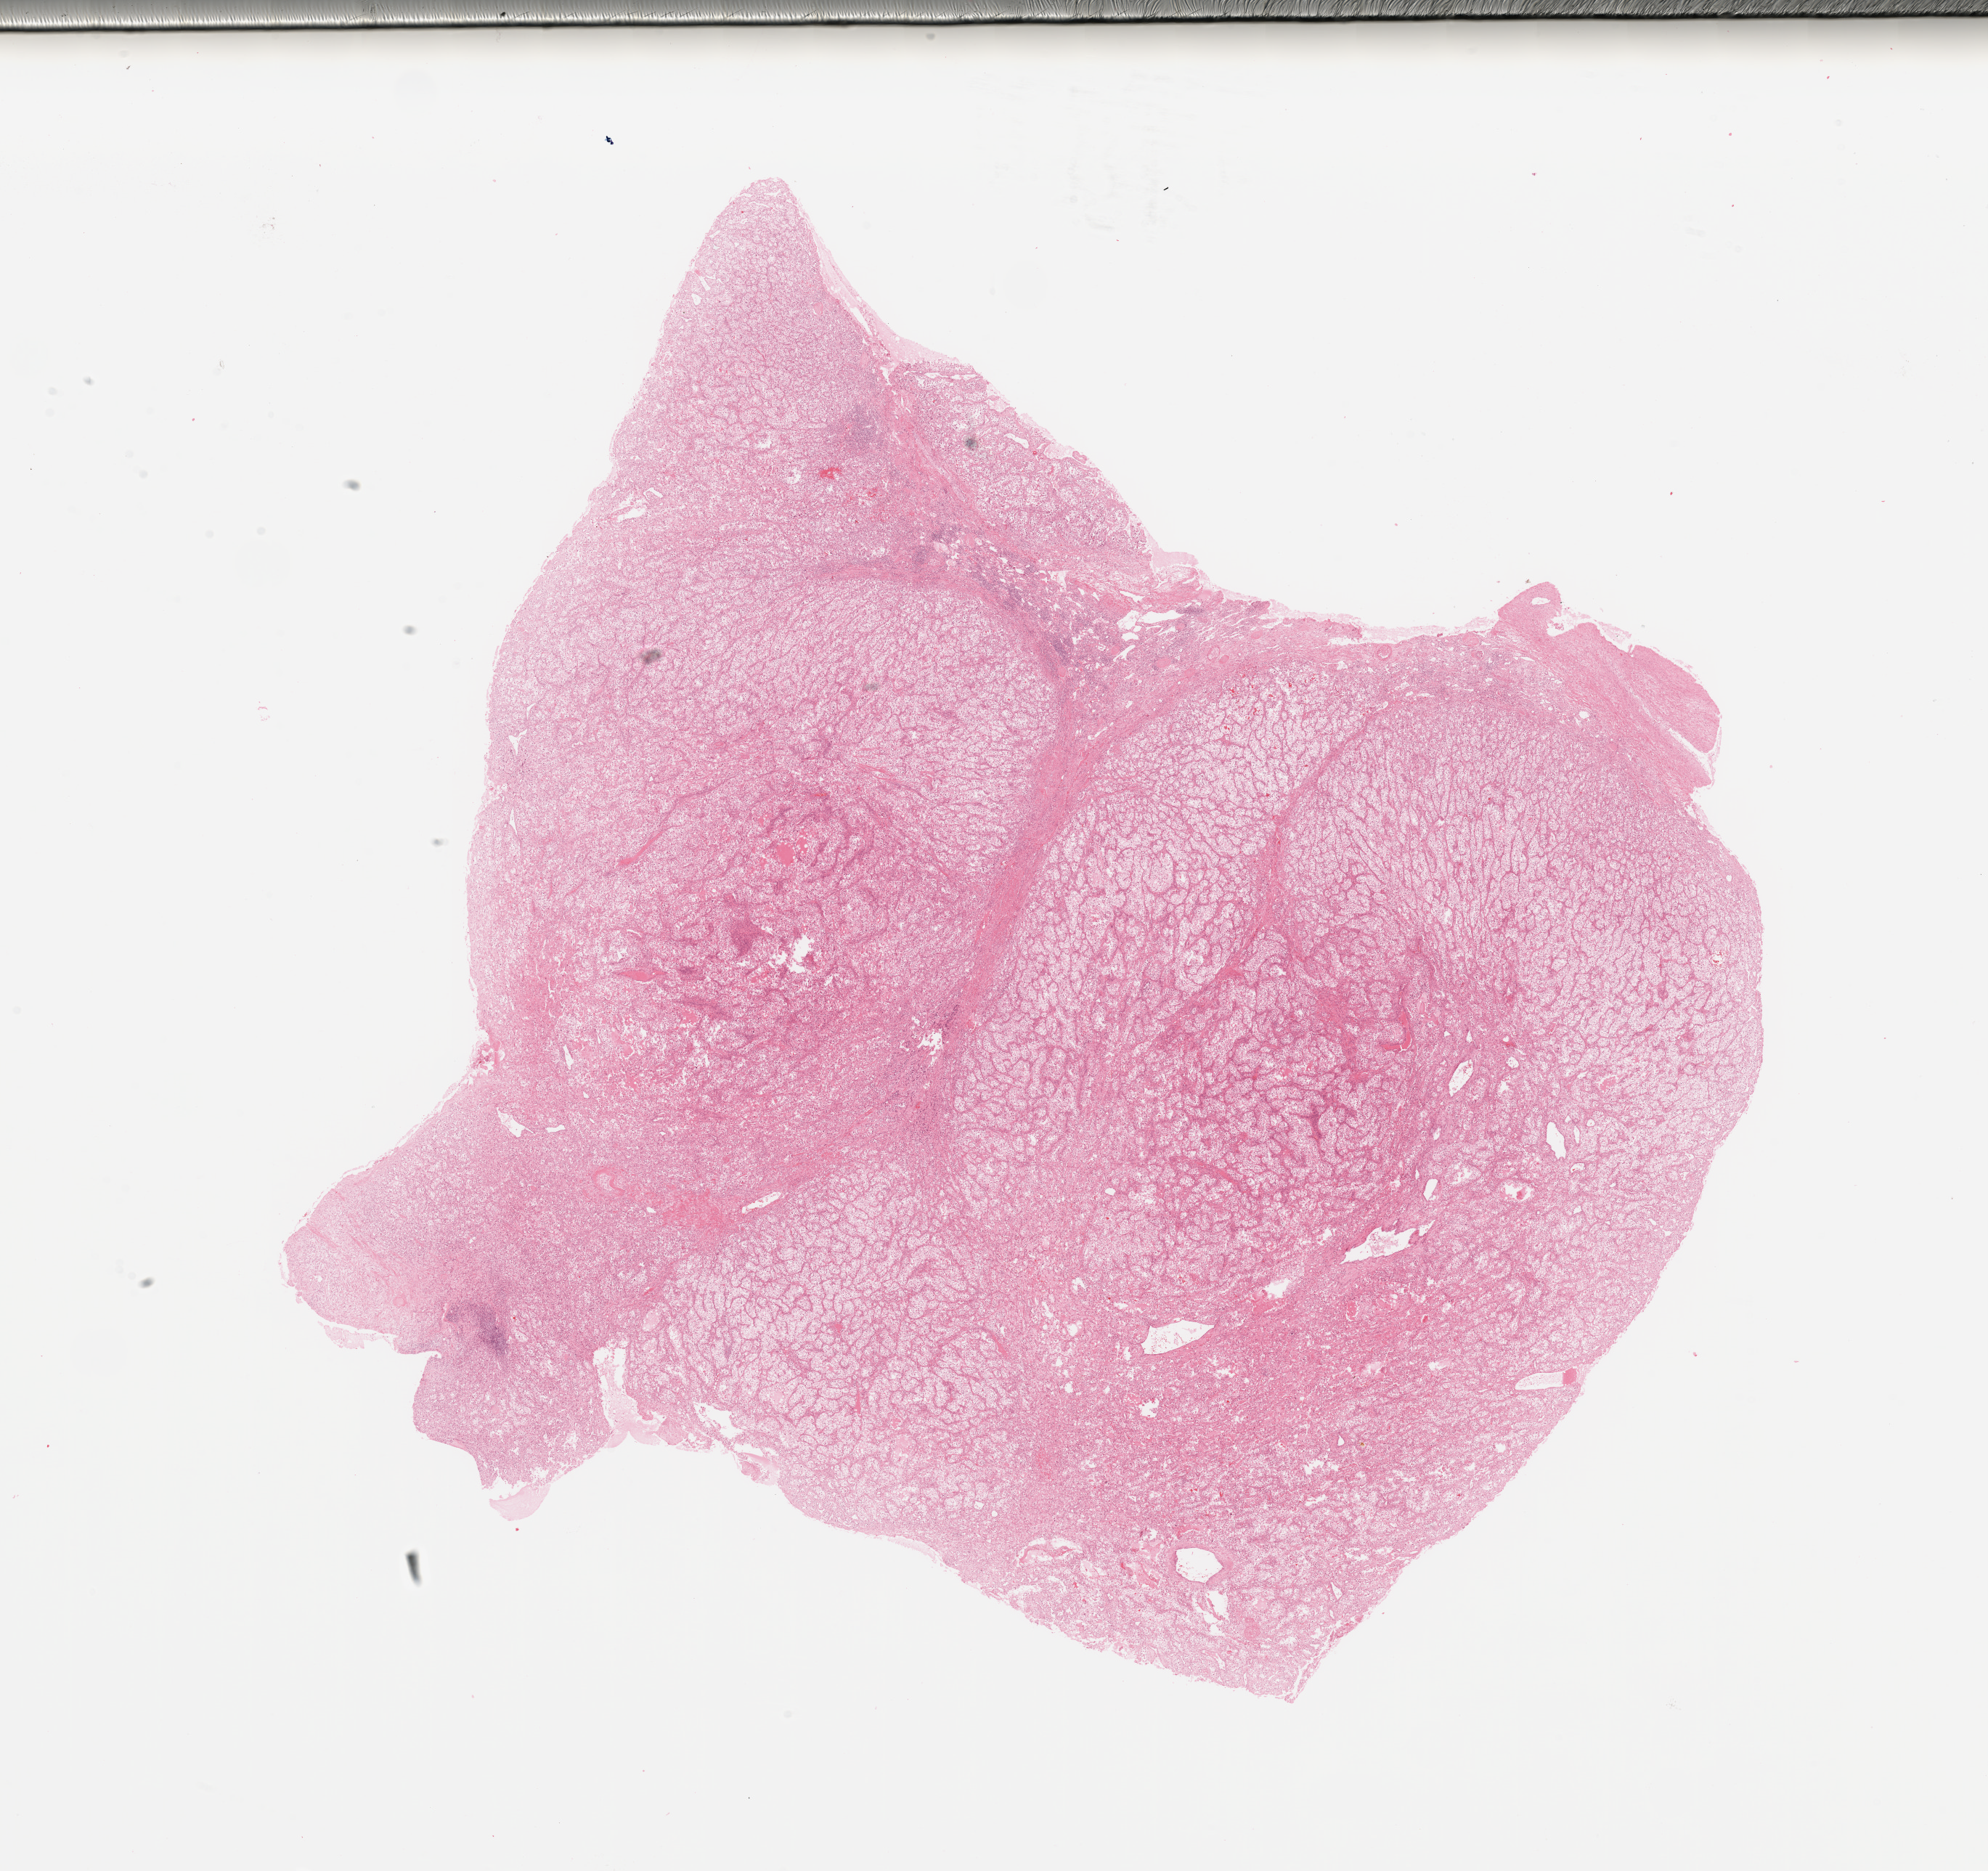
H&E-stained whole-slide image, shown as a low-resolution overview of the whole scanned area (about 21.7 x 20.4 mm). Tumour tissue sample, sampled site: kidney. 60-year-old male patient. Histologic grade: G3 (poorly differentiated). Slide review estimates, as recorded: tumour nuclei 85%, necrosis 5%.
Histologic diagnosis: Renal cell carcinoma, NOS.